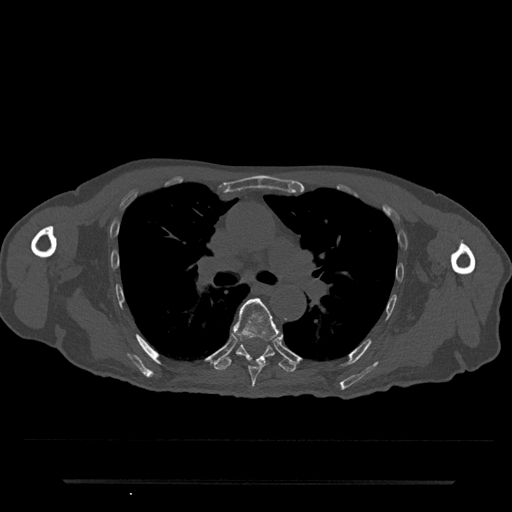
CT including the spine, one axial slice; position 509 of 797 along the scan axis; 120 kVp; bone window (W 1800 / L 400 HU); 0.5 mm slice thickness; 512 × 512 image matrix. Male patient, age 74 years. Case-level facts recorded for this patient, not image findings: primary cancer: prostate.
Structures marked on this image (semi-automatic segmentation, software-assisted and operator-edited):
- T6 vertebra: bounding box (x1, y1, x2, y2) in pixels: (233, 298, 280, 388)
- T7 vertebra: (215, 344, 296, 372)